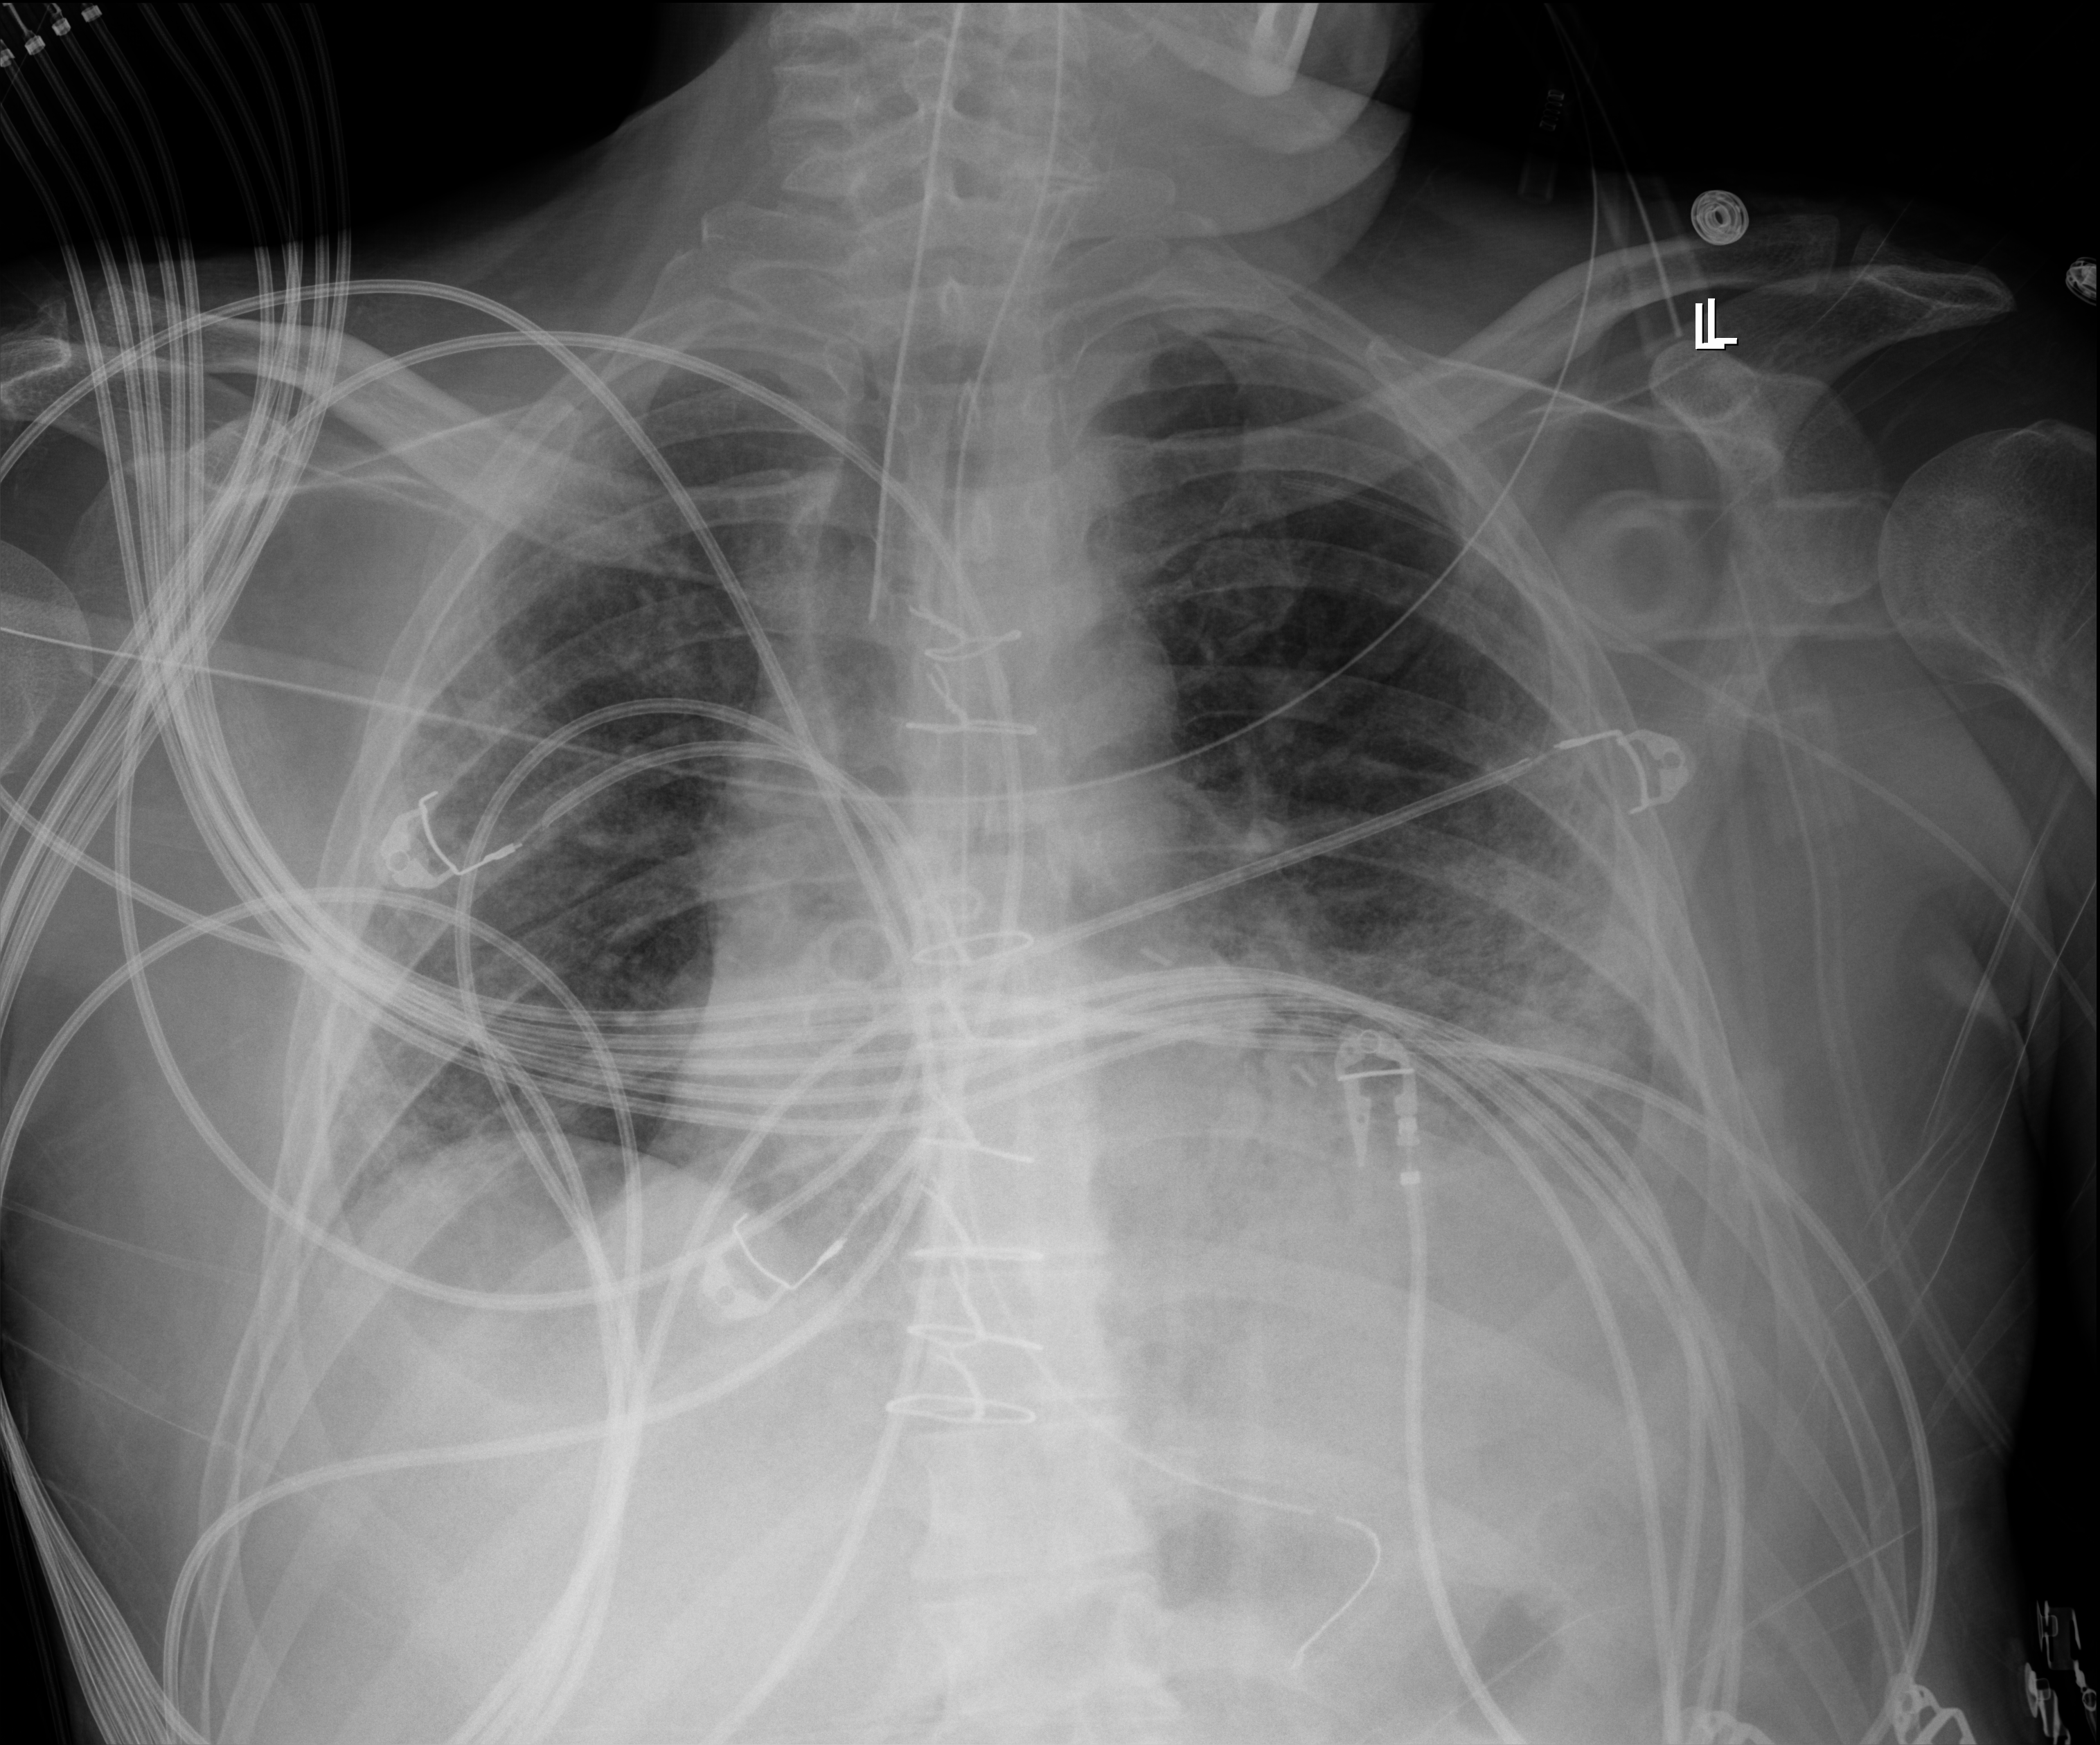
Bedside chest radiograph (digital radiography); anteroposterior (AP) projection. Male patient hospitalised with COVID-19, age 18–59 years.
Admission-level facts for this patient (not findings on this image; timing relative to this image not recorded): admitted to intensive care during this hospital stay: yes; length of hospital stay: 63 days; mechanically ventilated during this hospital stay: yes.